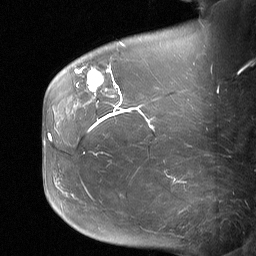
Breast MRI (dynamic contrast-enhanced), one sagittal slice; slice 18 of 64 in the series (ordered by position); dynamic contrast-enhanced study with each time point stored as its own series, time point 2 of 3 at this slice position (early post-contrast, ordered by acquisition time); 1.5 T; TE 4.8 ms, TR 27 ms; 256 × 256 image matrix. Female patient, age 60 years. From the clinical record (not read from this slice): setting: breast cancer imaged before/during neoadjuvant chemotherapy; receptor status: HR-positive, HER2-negative.
Outlined on this slice (semi-automatically segmented with operator editing):
- analysis volume of interest (the breast-tissue region the enhancement analysis was run in; not a lesion): bounding box [x1, y1, x2, y2] px = [79, 50, 122, 99]
- tumour enhancement mask (voxels above the 90 % enhancement threshold inside the analysis volume of interest): [79, 69, 120, 94]